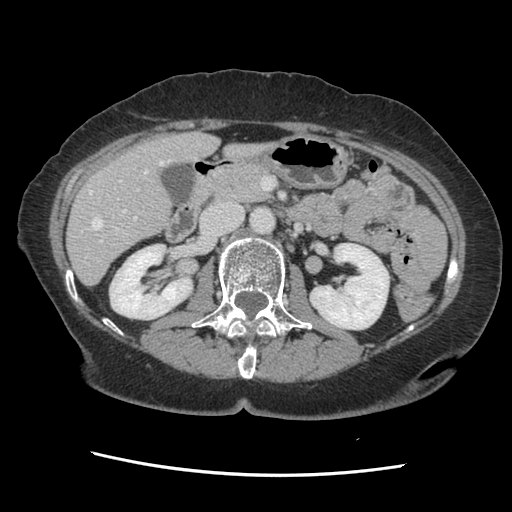
Contrast-enhanced abdominal CT, one axial slice. Slice 65 of 141 in the series (ordered by position). 120 kVp. Soft-tissue window (W 400 / L 40 HU). 2.5 mm slice thickness. 512 × 512 image matrix. Female patient, age 61 years. Case-level facts recorded for this patient, not image findings: diagnosis: colorectal cancer liver metastases, imaged before liver resection; multiple liver metastases: no; largest metastasis: 2.4 cm.
Structures marked on this image (manually delineated by an expert):
- hepatic veins: bounding box [x1, y1, x2, y2] px = [89, 159, 171, 229]
- liver: [68, 133, 266, 284]
- planned liver remnant (the part of the liver to remain after resection): [68, 133, 267, 284]
- portal vein (with intrahepatic branches): [101, 180, 139, 242]